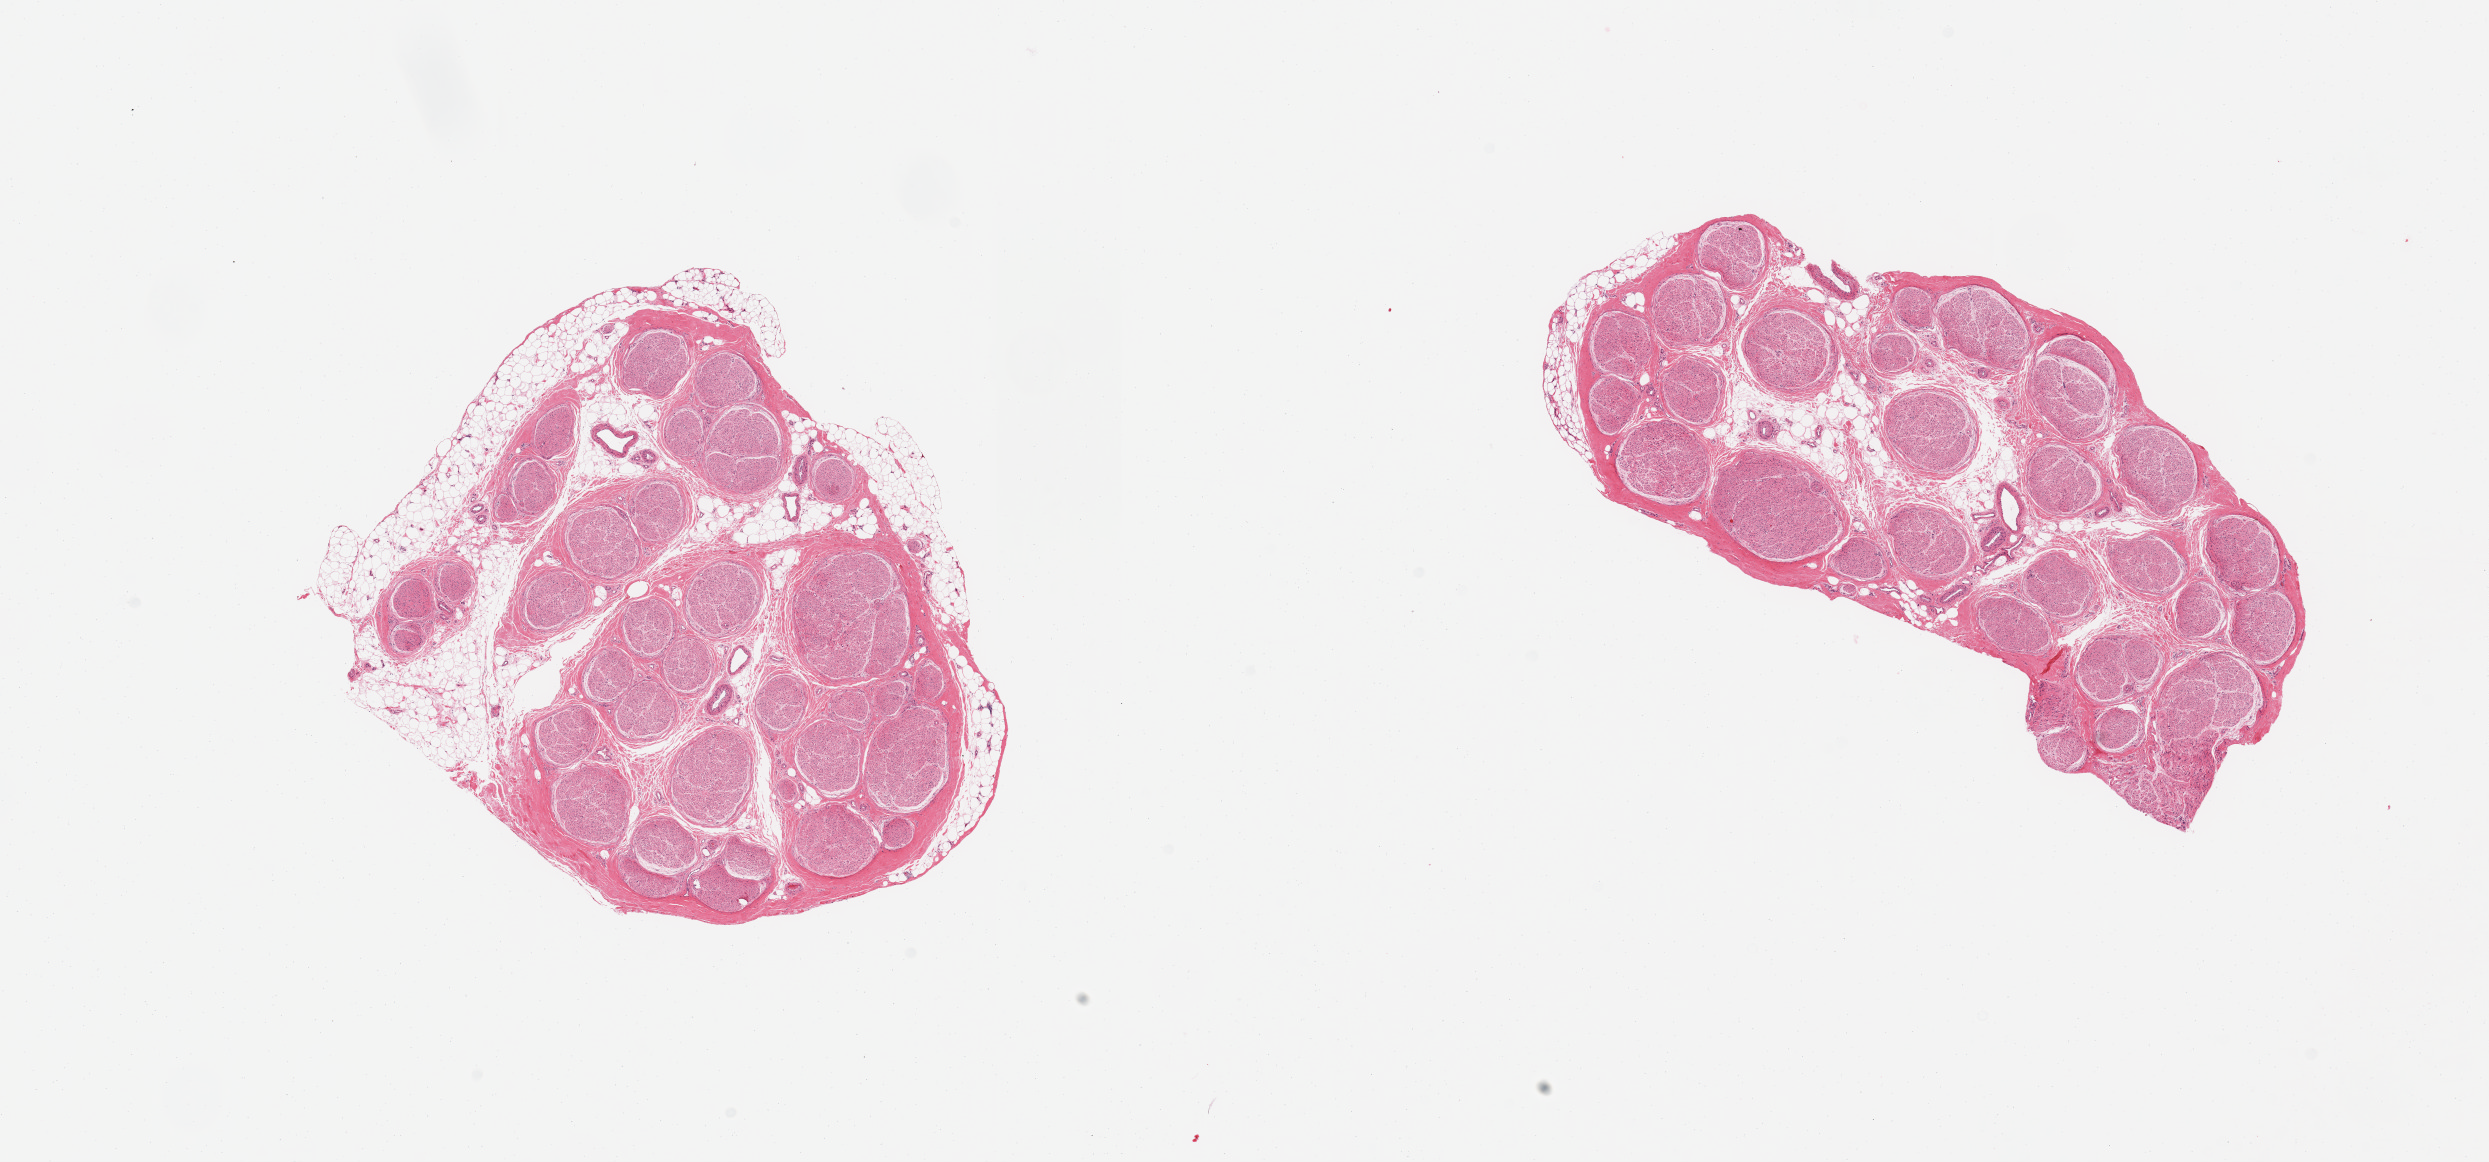
H&E whole-slide image, brightfield, whole scanned area (about 19.7 x 9.2 mm, acquisition: 20x scan) shown as a low-resolution overview; PAXgene-fixed, paraffin-embedded tissue; section of tibial nerve (target tissue); tissue donor sample. Male donor.
Review note (as recorded): 2 pieces; 10 & 20 % internal & external fat.